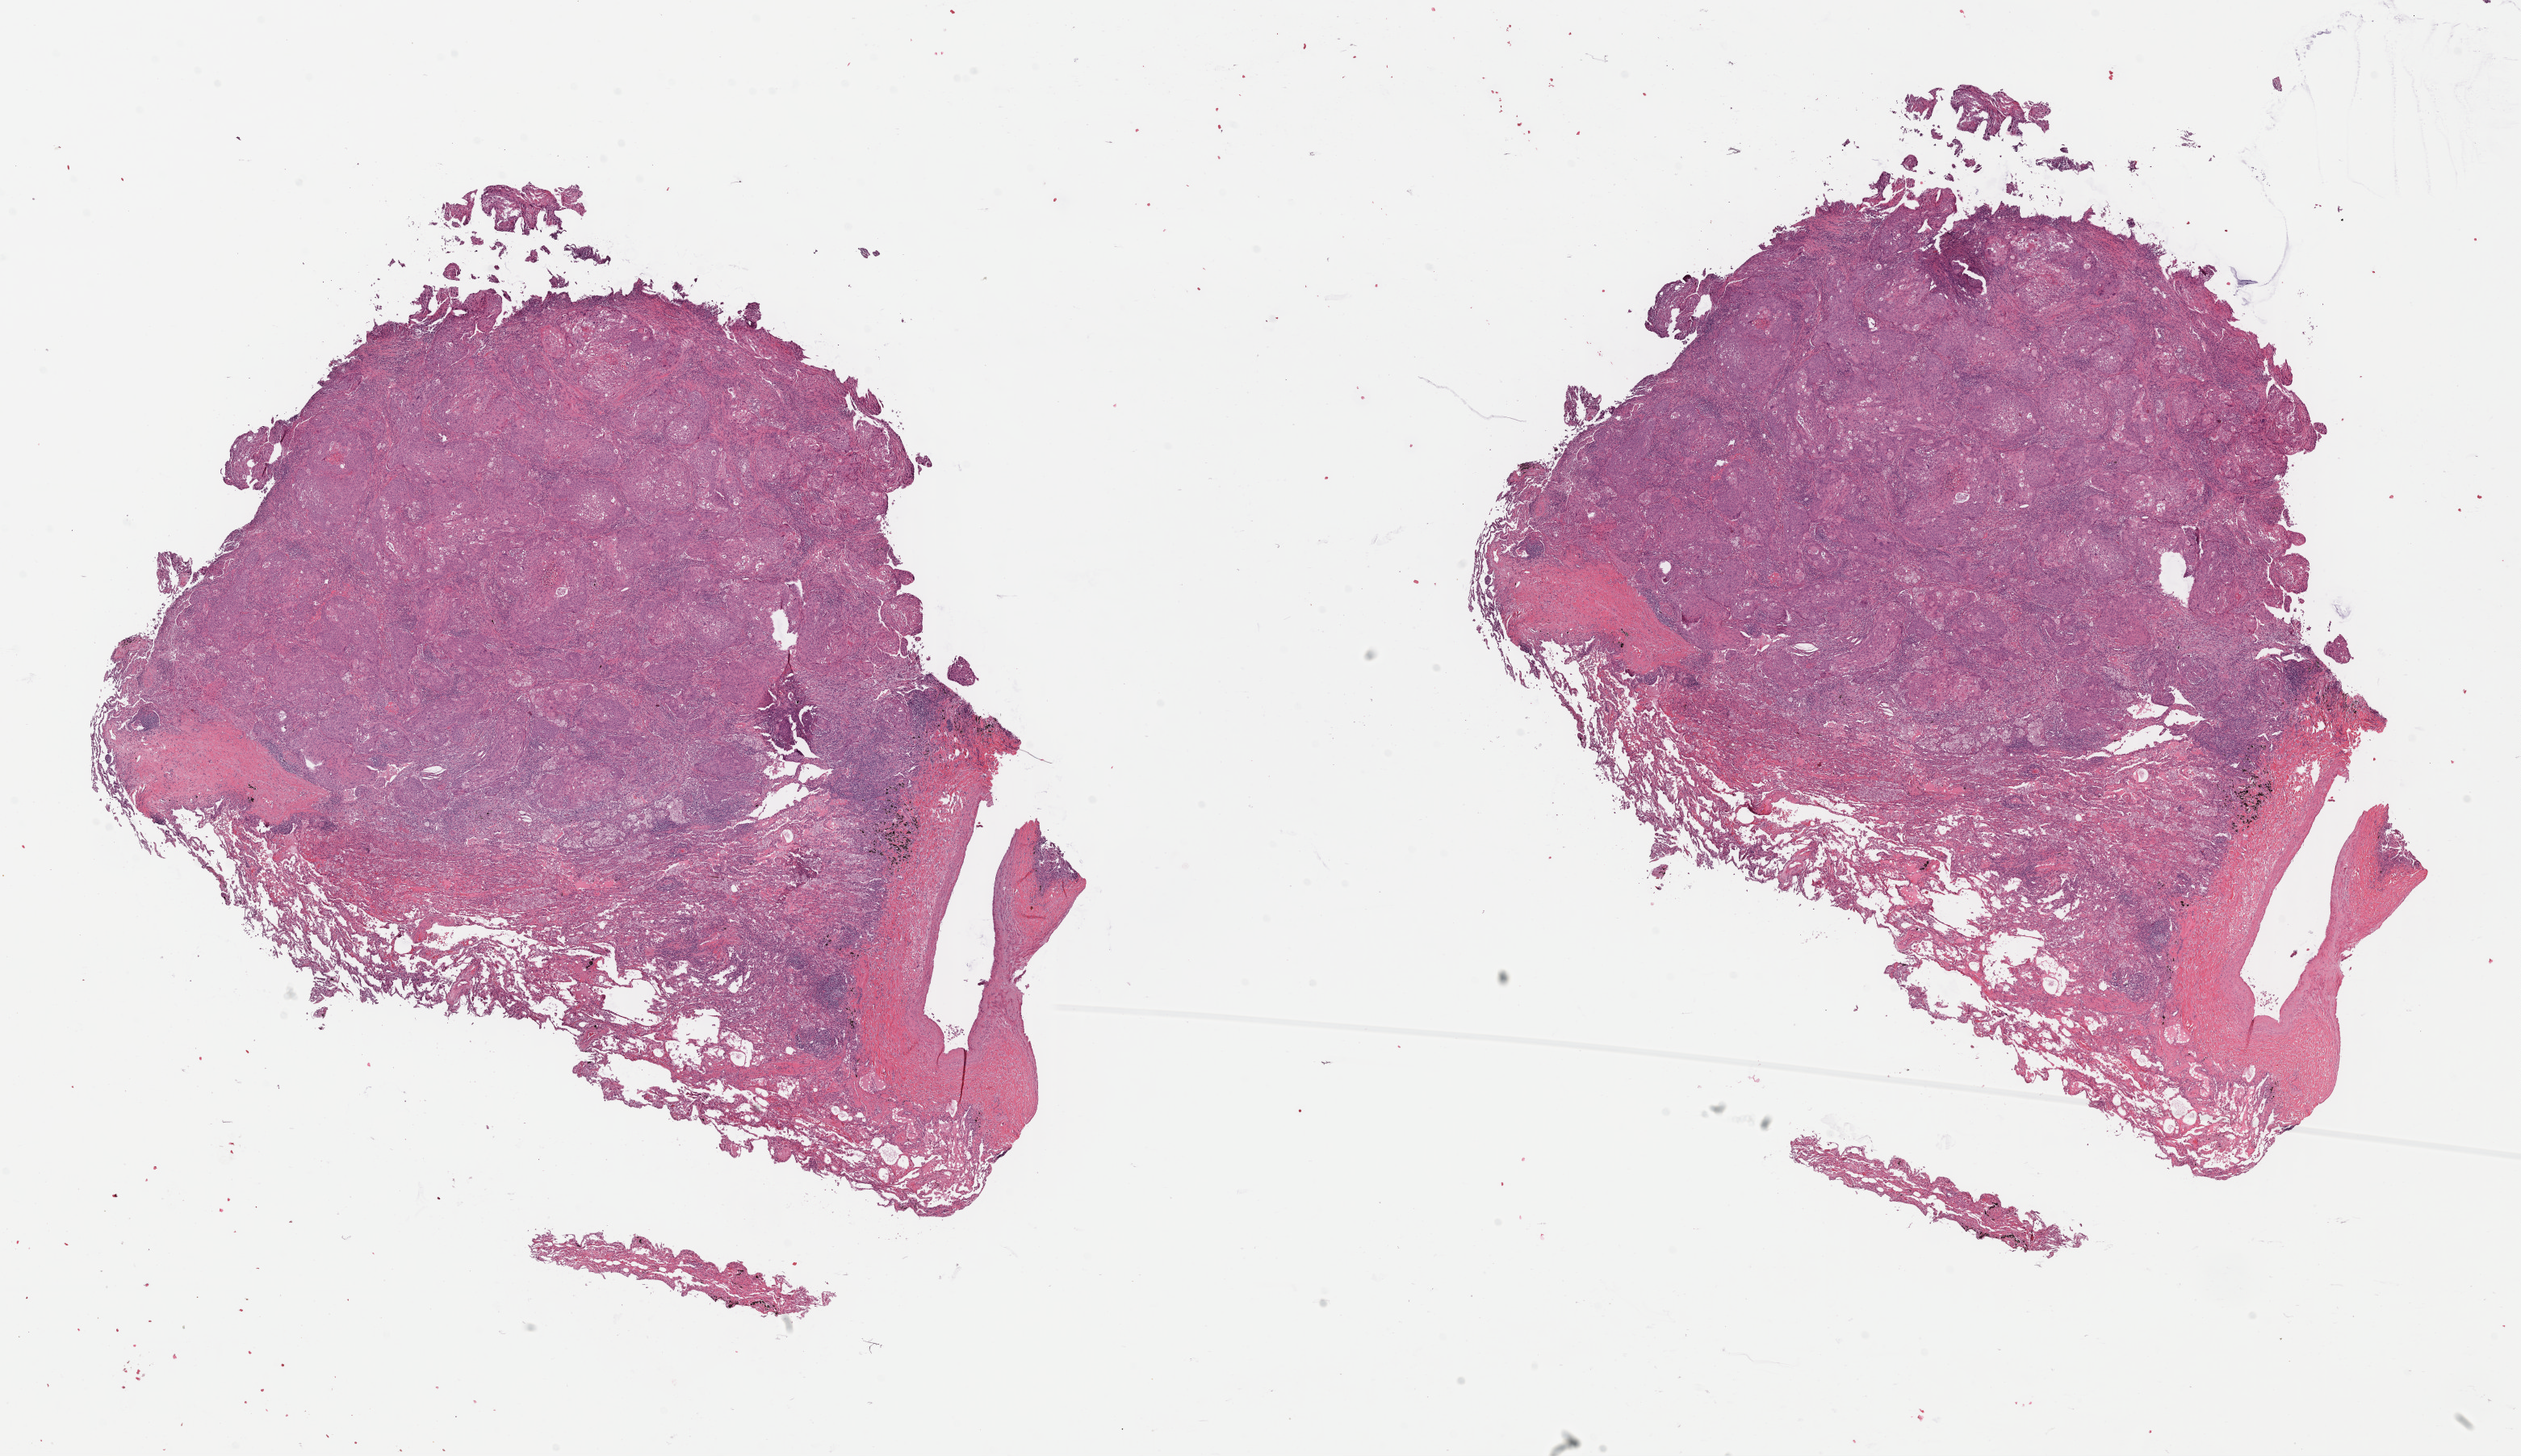
H&E whole-slide image — whole scanned area (about 24.6 x 14.2 mm) shown as a low-resolution overview. Formalin-fixed paraffin-embedded (FFPE) diagnostic section. Primary tumour sample from the lung. Patient: male, age at initial diagnosis 77 years.
* AJCC pathologic stage: IB (7th edition)
* histologic diagnosis: Squamous cell carcinoma, NOS (upper lobe, lung)